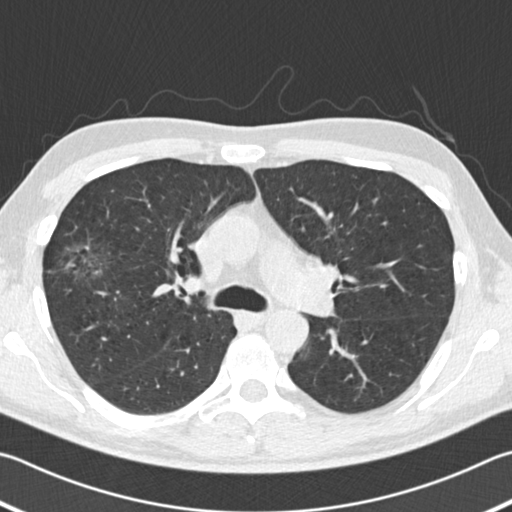
Axial slice from a low-dose chest CT screening exam, second screening round (one year after baseline), lung window (W 1500 / L -600 HU), slice 63 of 182 in the series. Male participant, aged 56 years at enrolment. Former smoker at enrolment.
Expert-annotated lung lesion, bounding box (x1, y1, x2, y2) in pixels: (43, 231, 122, 297). Reader record for this screening exam (exam-level; its link to the box is not recorded): non-calcified nodule or mass ≥4 mm, right upper lobe, 18 × 14 mm, spiculated (stellate) margins, soft tissue attenuation, pre-existing on the prior screen: yes; interval growth: yes. Official screen result: positive, other. Participant outcome: lung cancer diagnosed 42 days after this screen — bronchiolo-alveolar adenocarcinoma, NOS, right upper lobe, well differentiated (G1), stage IIB (AJCC 6th edition), 30 mm at pathology.